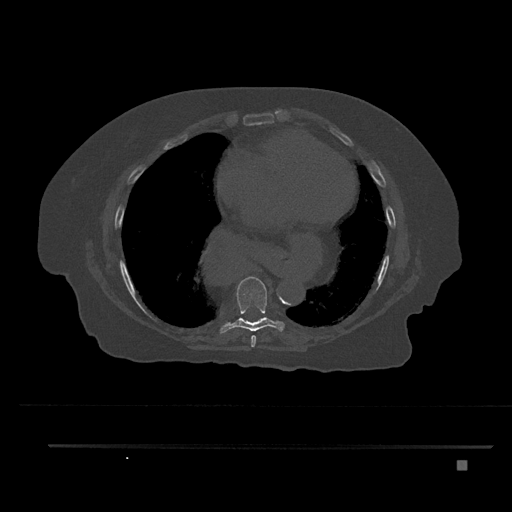
CT including the spine, one axial slice; position 445 of 797 along the scan axis; 120 kVp; bone window (W 1800 / L 400 HU); 512 × 512 image matrix, field of view 437 × 437 mm. Female patient, age 76 years. From the clinical record (not read from this slice): primary cancer: lung.
Annotated regions visible in this slice (semi-automatically segmented with operator editing):
- T7 vertebra: bounding box <251,335,256,347> (left, top, right, bottom; pixels)
- T8 vertebra: <219,276,285,334>